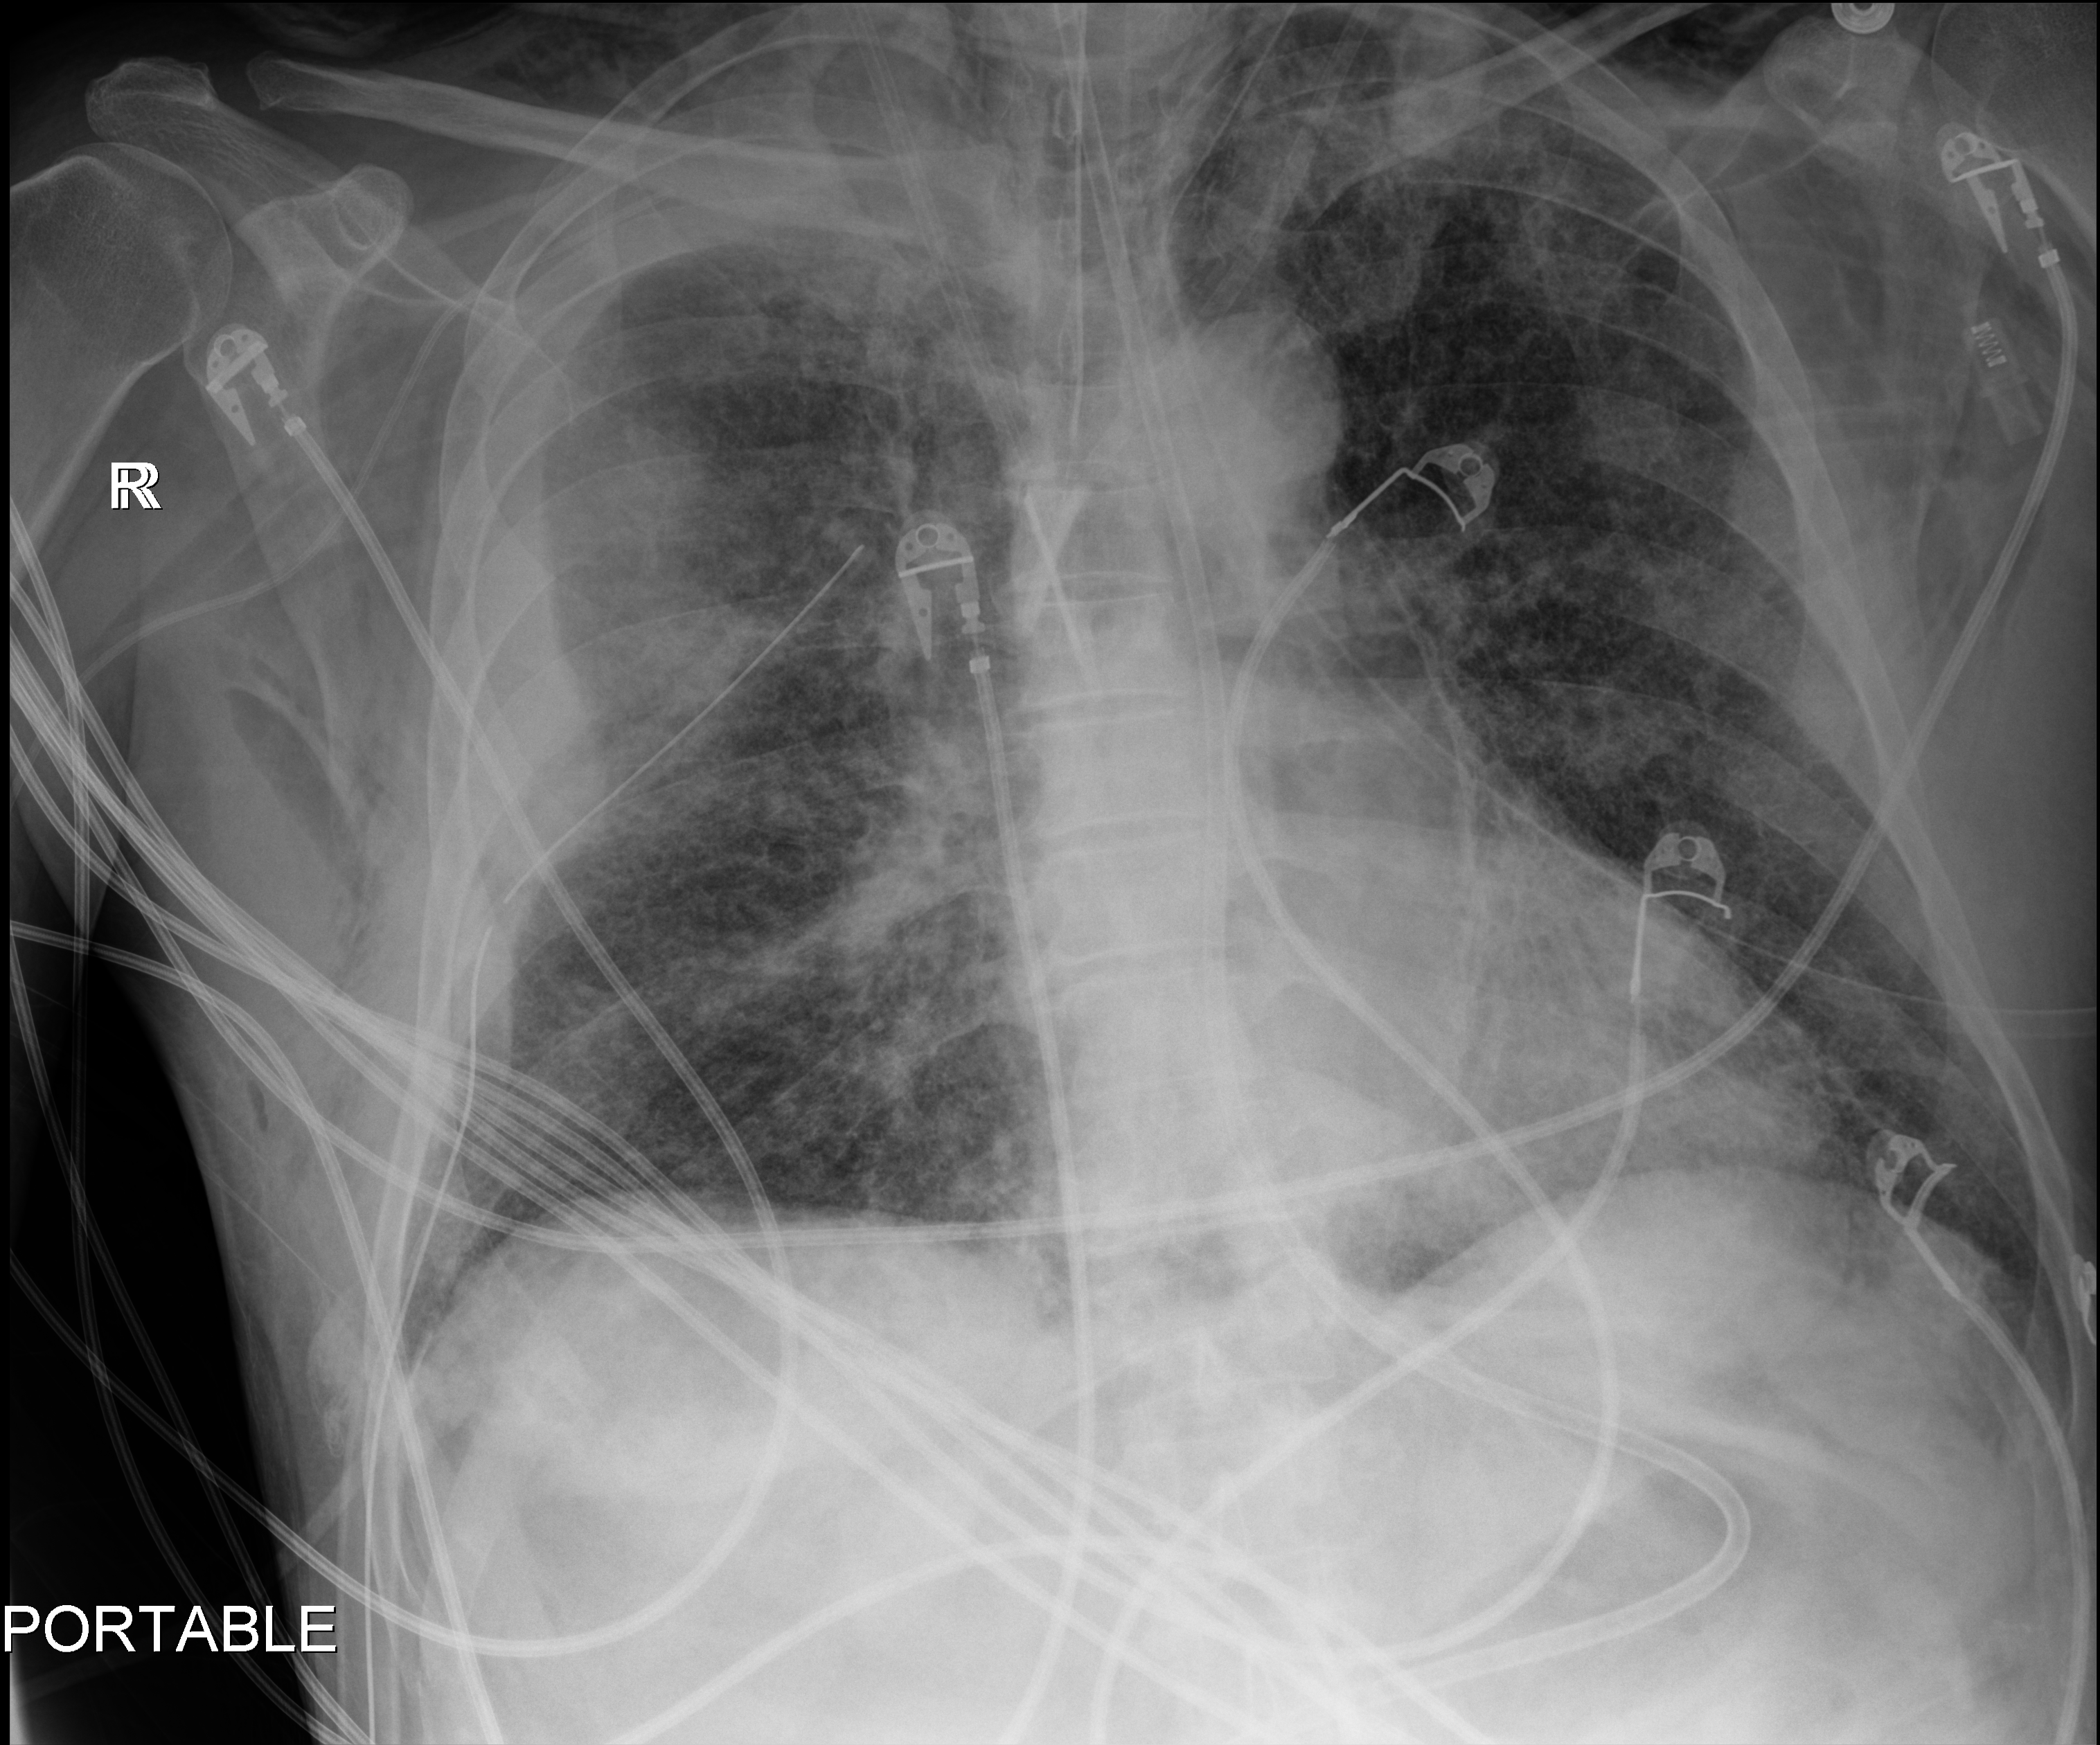
Portable chest radiograph, anteroposterior (AP) projection. Male patient hospitalised with COVID-19, age 18–59 years.
Admission-level facts for this patient (not findings on this image; timing relative to this image not recorded):
- mechanically ventilated during this hospital stay: yes
- admitted to intensive care during this hospital stay: yes
- length of hospital stay: 42 days